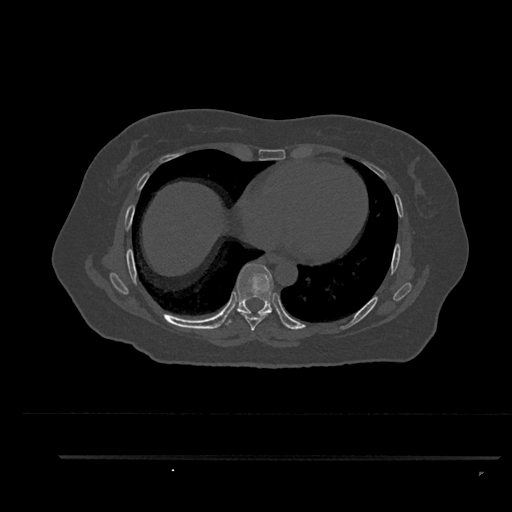
CT including the spine, one axial slice. Position 484 of 797 along the scan axis. 120 kVp. Bone window (W 1800 / L 400 HU). 0.5 mm slice thickness. 512 × 512 image matrix, field of view 408 × 408 mm. Patient: female, 44 years. From the clinical record (not read from this slice): primary cancer: renal; vertebrae with lytic lesions (as recorded): L1.
Structures marked on this image (semi-automatically segmented with operator editing):
- T7 vertebra: box from (x=240, y=311) to (x=269, y=334) px
- T8 vertebra: (x=225, y=264)–(x=282, y=326)